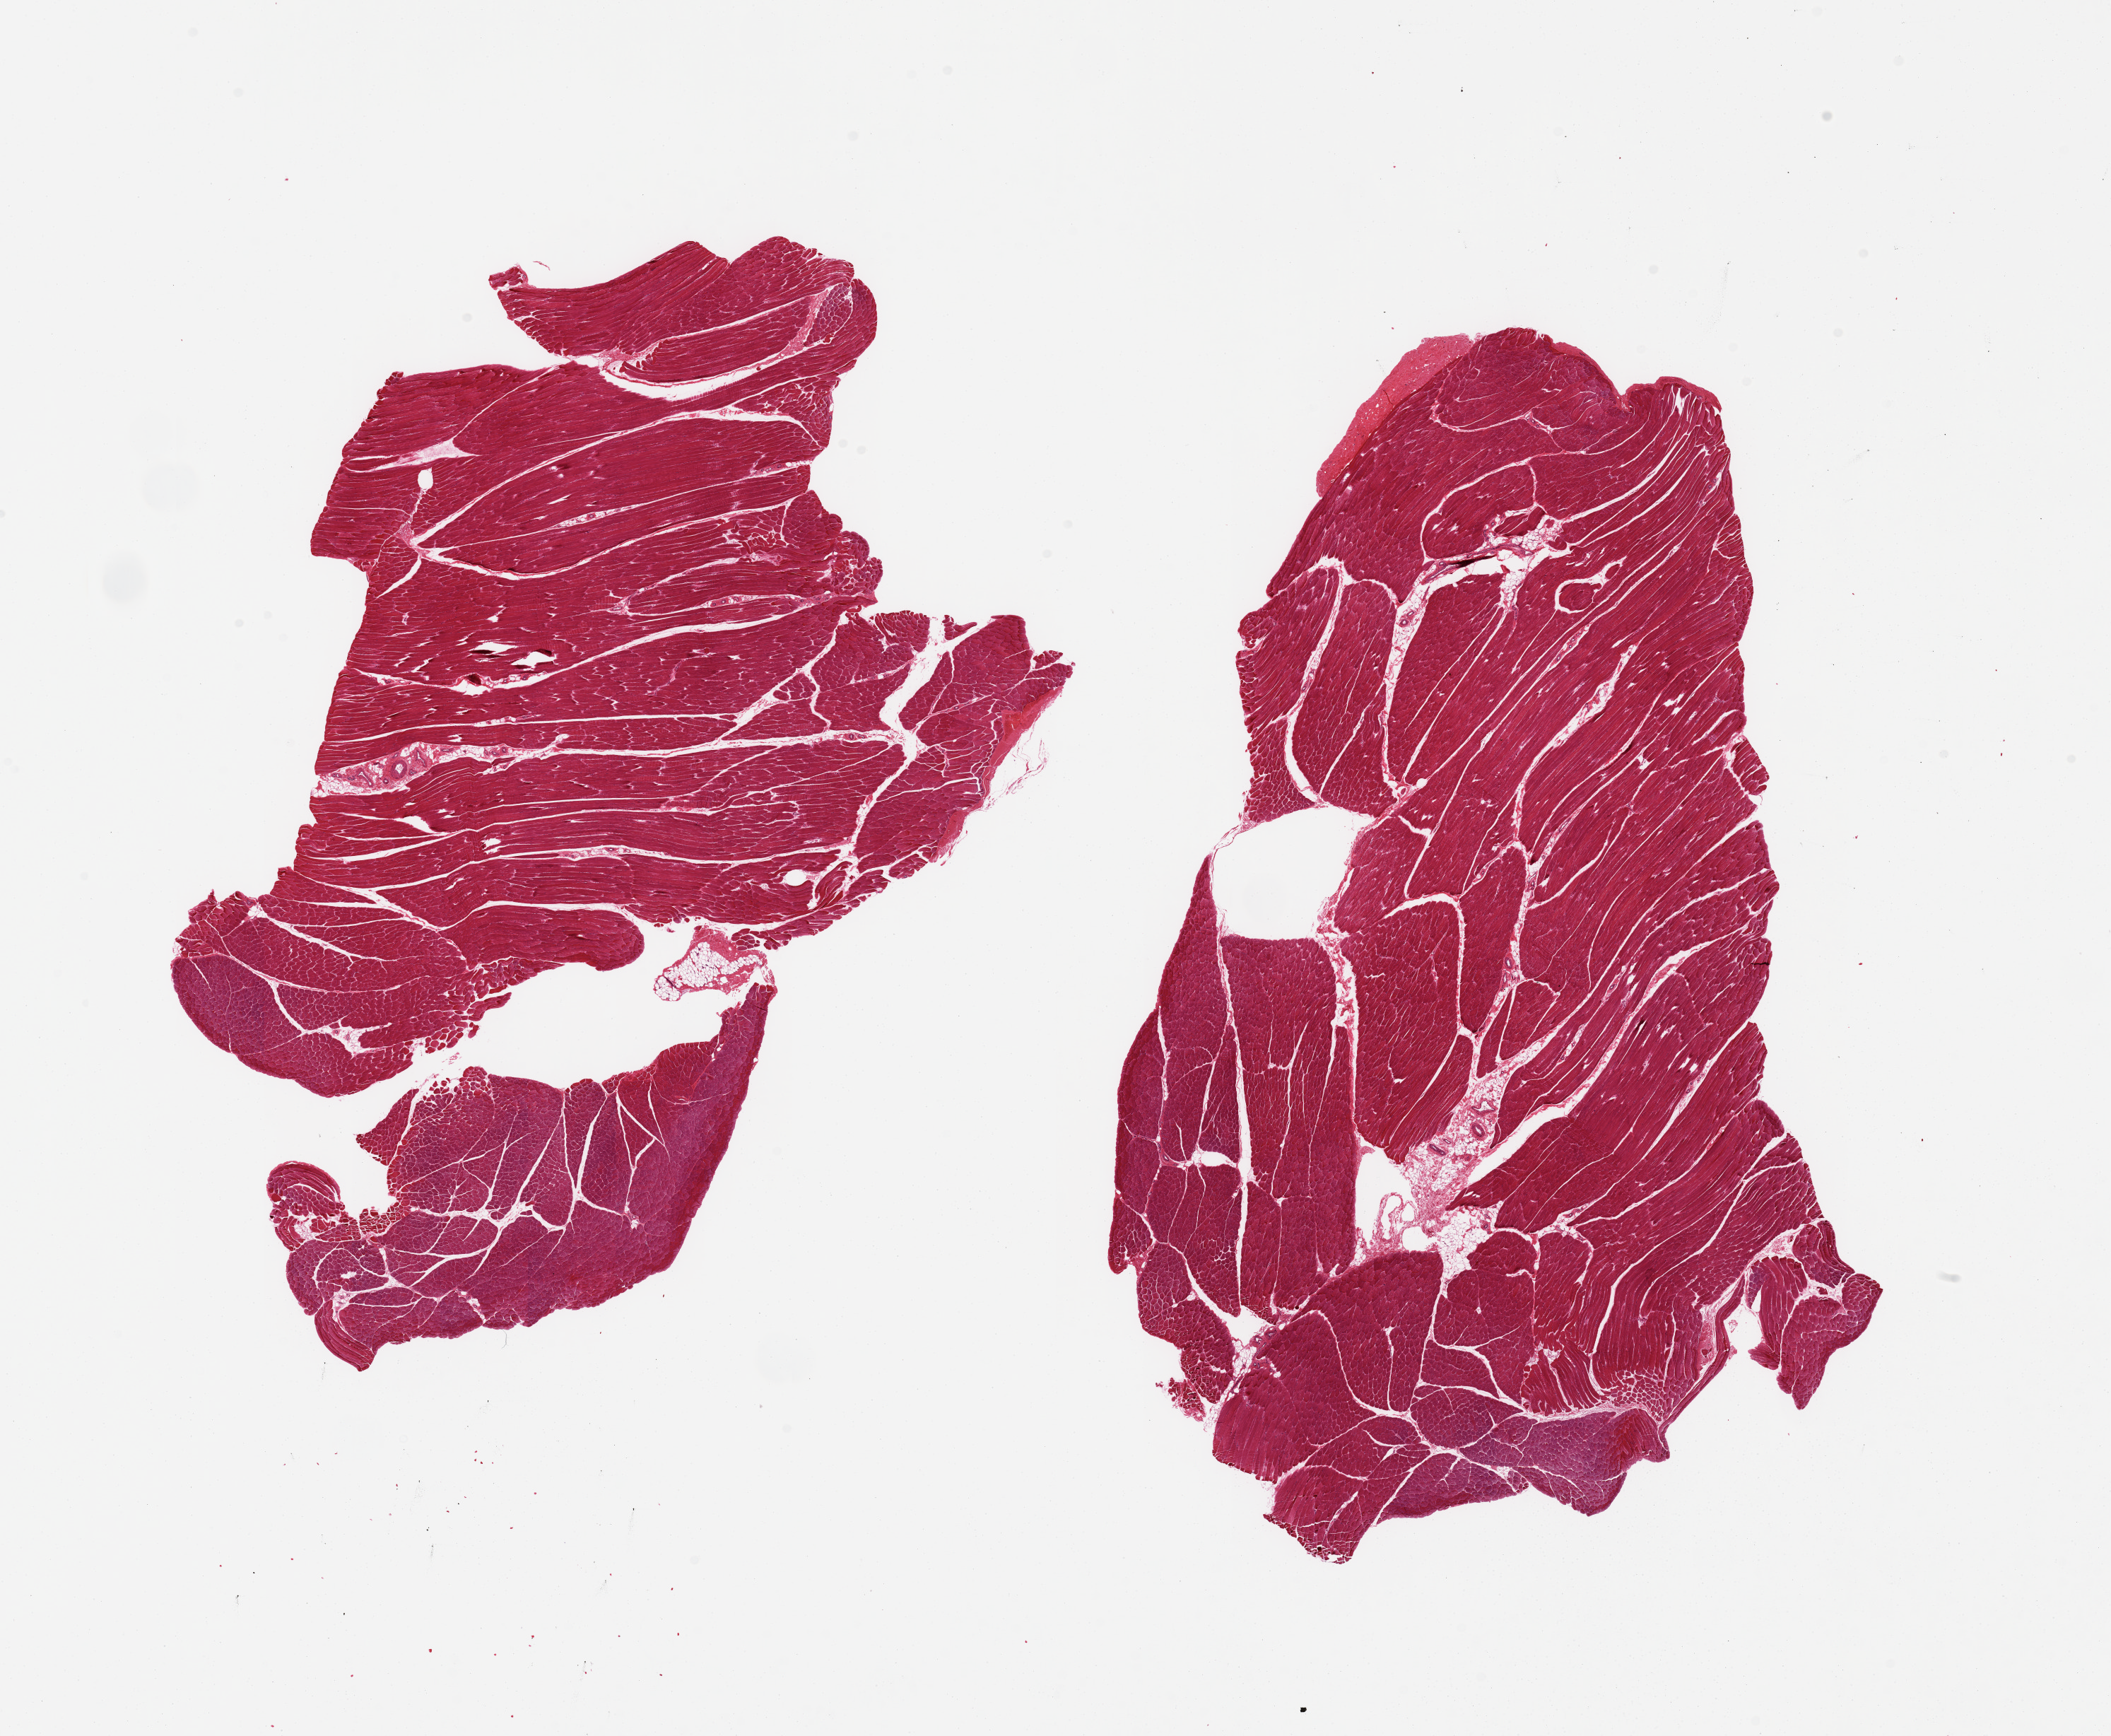
Digitized hematoxylin and eosin (H&E)-stained section, brightfield — shown as a low-resolution overview of the whole scanned area (about 23.6 x 19.4 mm), PAXgene-fixed paraffin-embedded (PFPE) section, section of skeletal muscle (target tissue), donor tissue sample. Donor: male.
- reviewer comment on this tissue sample: 2 pieces, skeletal muscle with attached portion of tendon